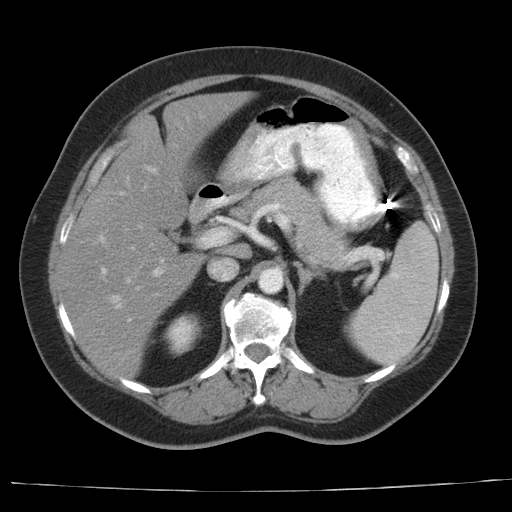
Contrast-enhanced abdominal CT, one axial slice. Slice 19 of 44 in the series (ordered by position). Reconstruction kernel AA-1. Intravenous contrast given. Soft-tissue window (W 400 / L 40 HU). 5 mm slice thickness. 512 × 512 image matrix, field of view 373 × 373 mm. Female patient. Case-level facts recorded for this patient, not image findings: diagnosis: colorectal cancer liver metastases, imaged before liver resection.
Outlined on this slice (outlined manually by an expert reader):
- hepatic veins: bounding box <111,192,123,308> (left, top, right, bottom; pixels)
- liver: <58,92,250,380>
- planned liver remnant (the part of the liver to remain after resection): <108,92,251,227>
- portal vein (with intrahepatic branches): <99,167,161,322>